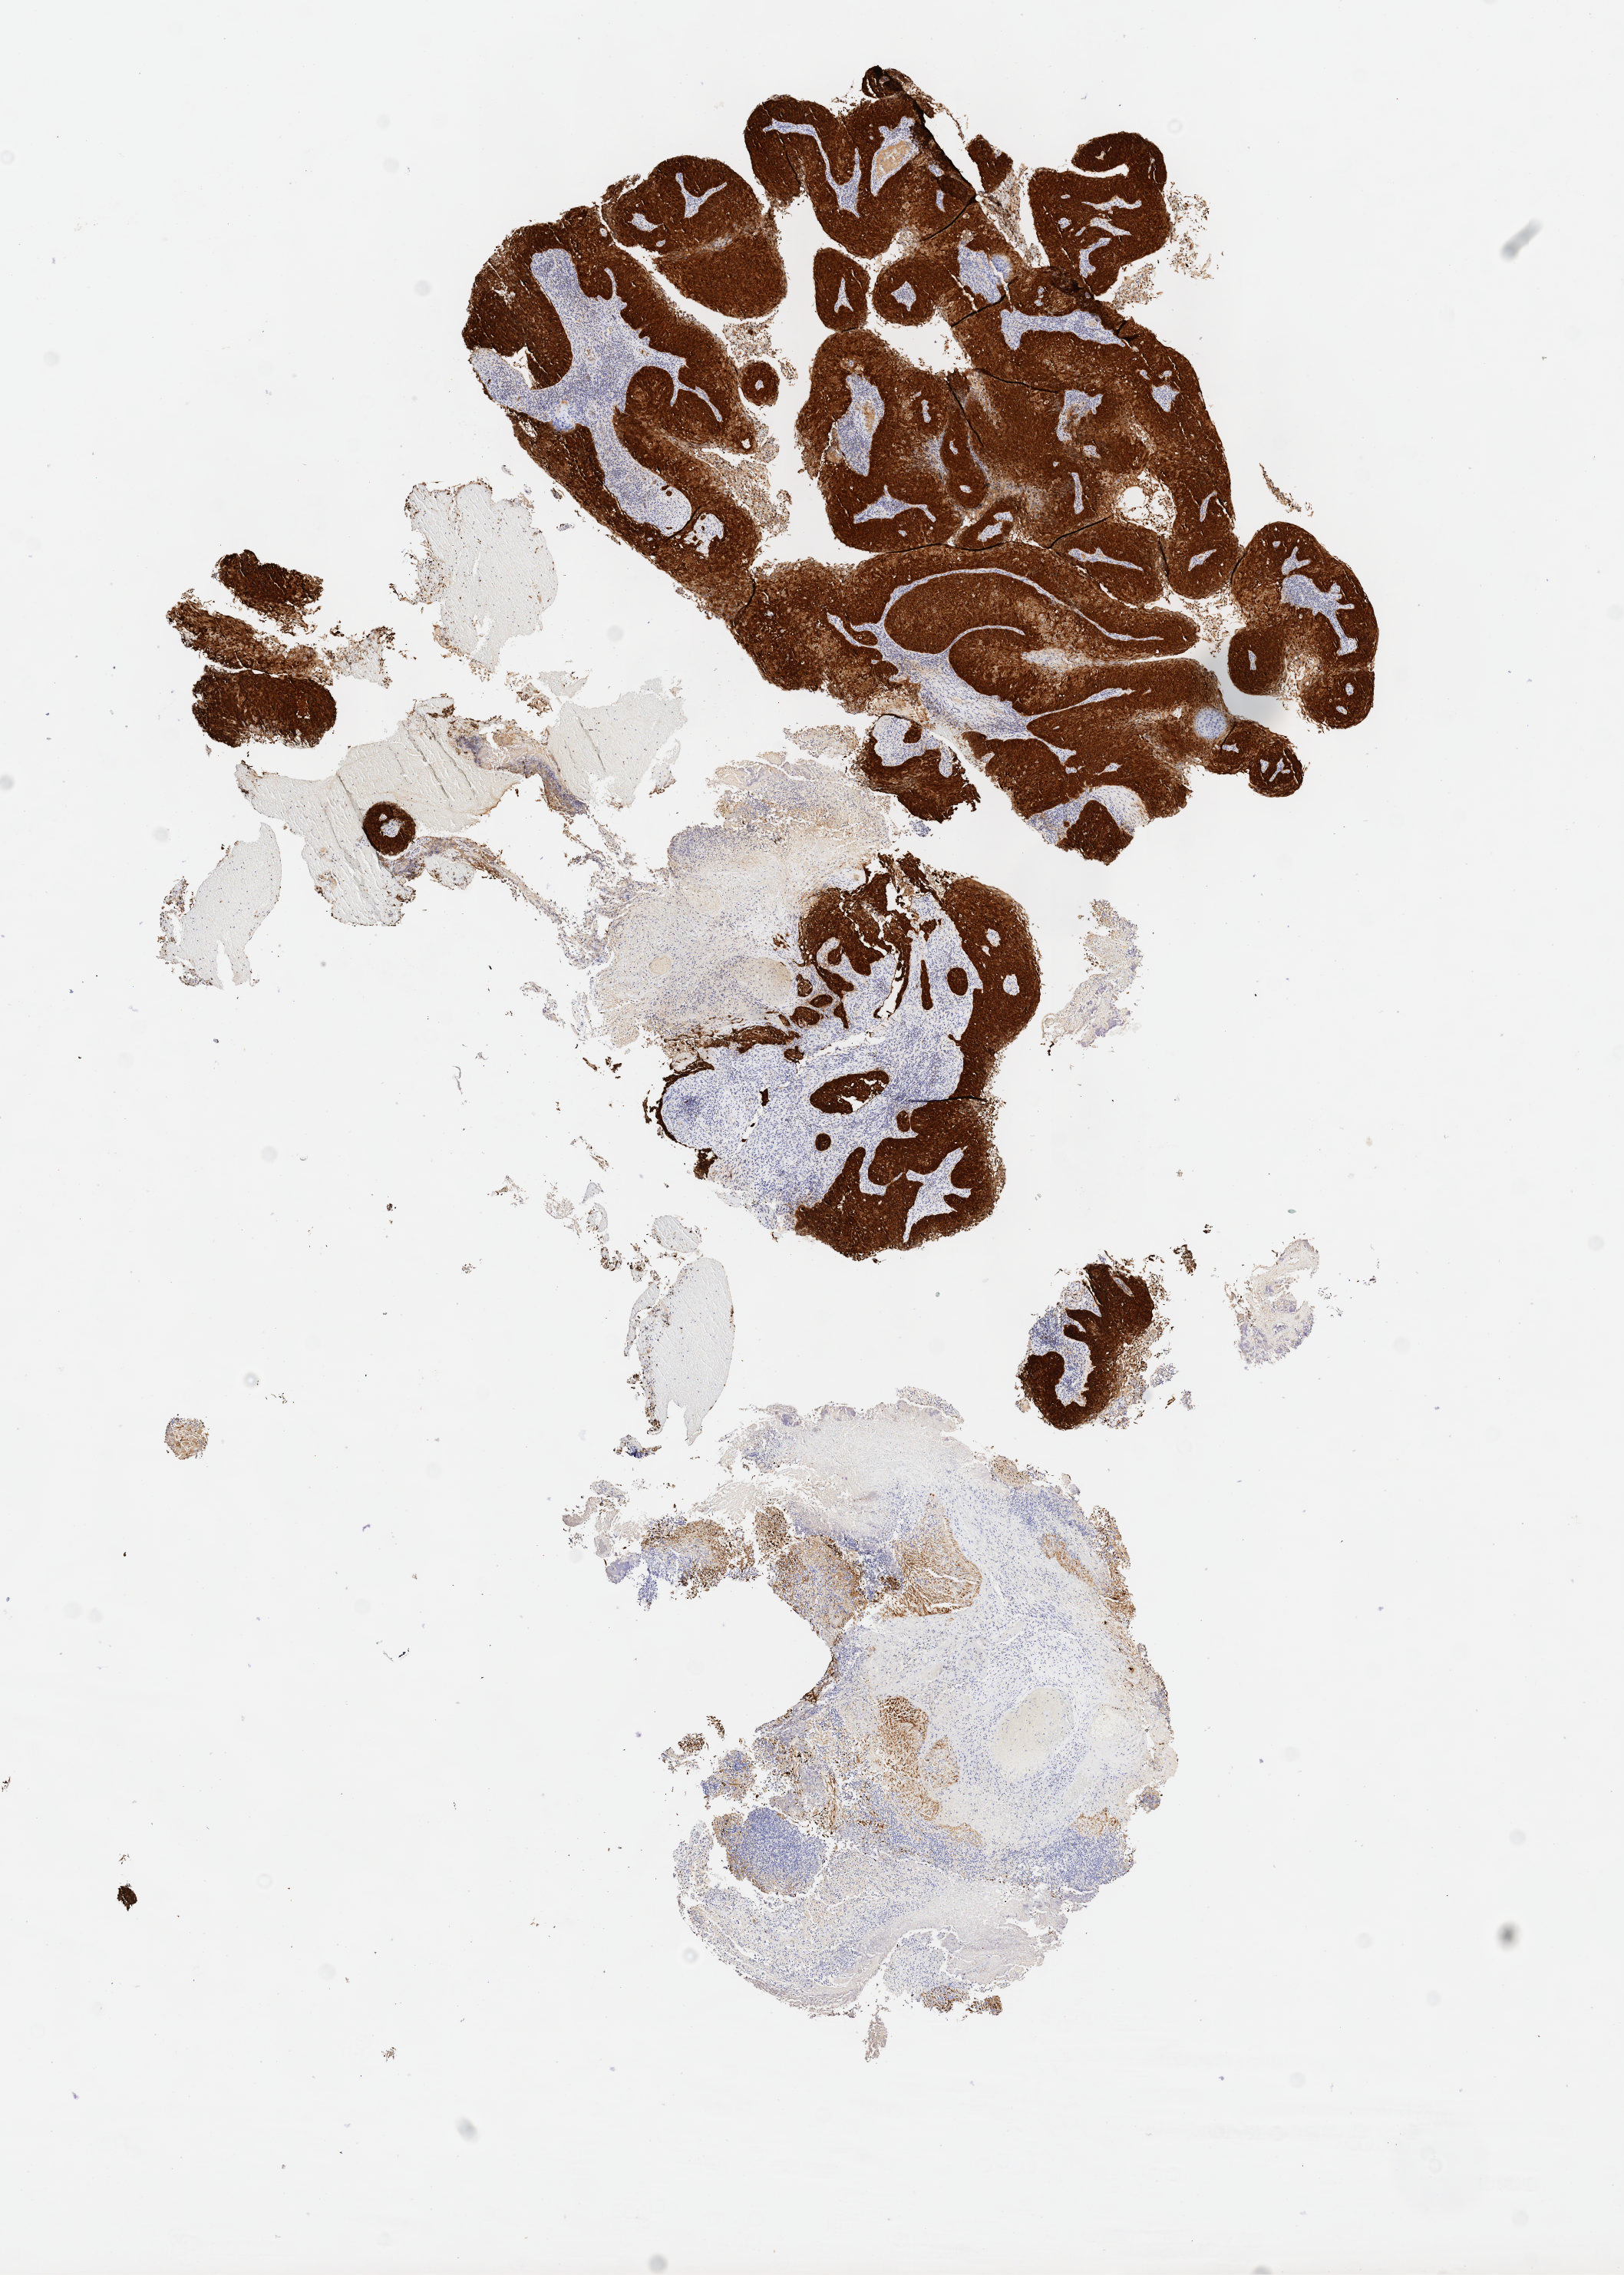
Whole-slide image, immunohistochemical stain for p16 (p16INK4a), whole scanned area (about 8.6 x 12.0 mm) shown as a low-resolution overview. Tumor tissue. Site: cervix. Patient: female, aged 46.
- diagnosis: Squamous cell carcinoma, large cell, nonkeratinizing, NOS